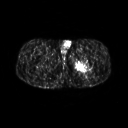
FDG PET of an extremity soft-tissue mass (from a PET/CT study), one axial slice; position 254 of 267 along the scan axis; 3.27 mm slice thickness; 128 × 128 image matrix. Male patient, age 27 years. From the clinical record (not read from this slice): histological type: extraskeletal osteosarcoma; grade: high; site of the primary tumour: left adductur.
Outlined on this slice (expert contour drawn on MRI and transferred to this co-registered scan by the dataset authors):
- gross tumour volume (mass): bounding box [x1, y1, x2, y2] px = [71, 55, 95, 74]